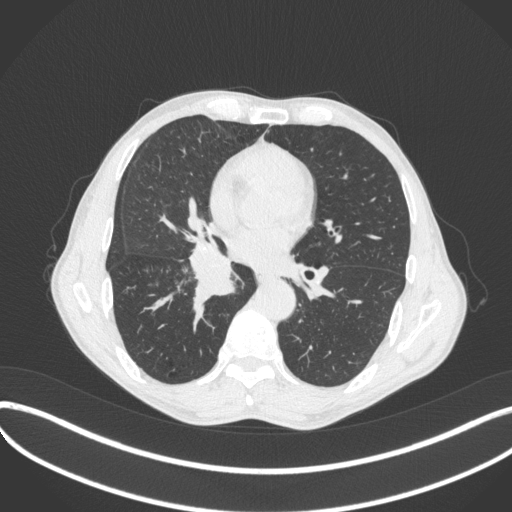
Chest CT, one axial slice; slice 209 of 481 in the series (ordered by position); reconstruction kernel B31f; 120 kVp; lung window (W 1500 / L -600 HU); 512 × 512 image matrix. Patient: male, 65 years. From the clinical record (not read from this slice): clinical TNM (as recorded): T2a N0 M0.
Outlined on this slice (bounding box drawn by a radiologist):
- lung tumour (recorded histology: squamous cell carcinoma): bounding box (x1, y1, x2, y2) in pixels: (183, 236, 240, 304)